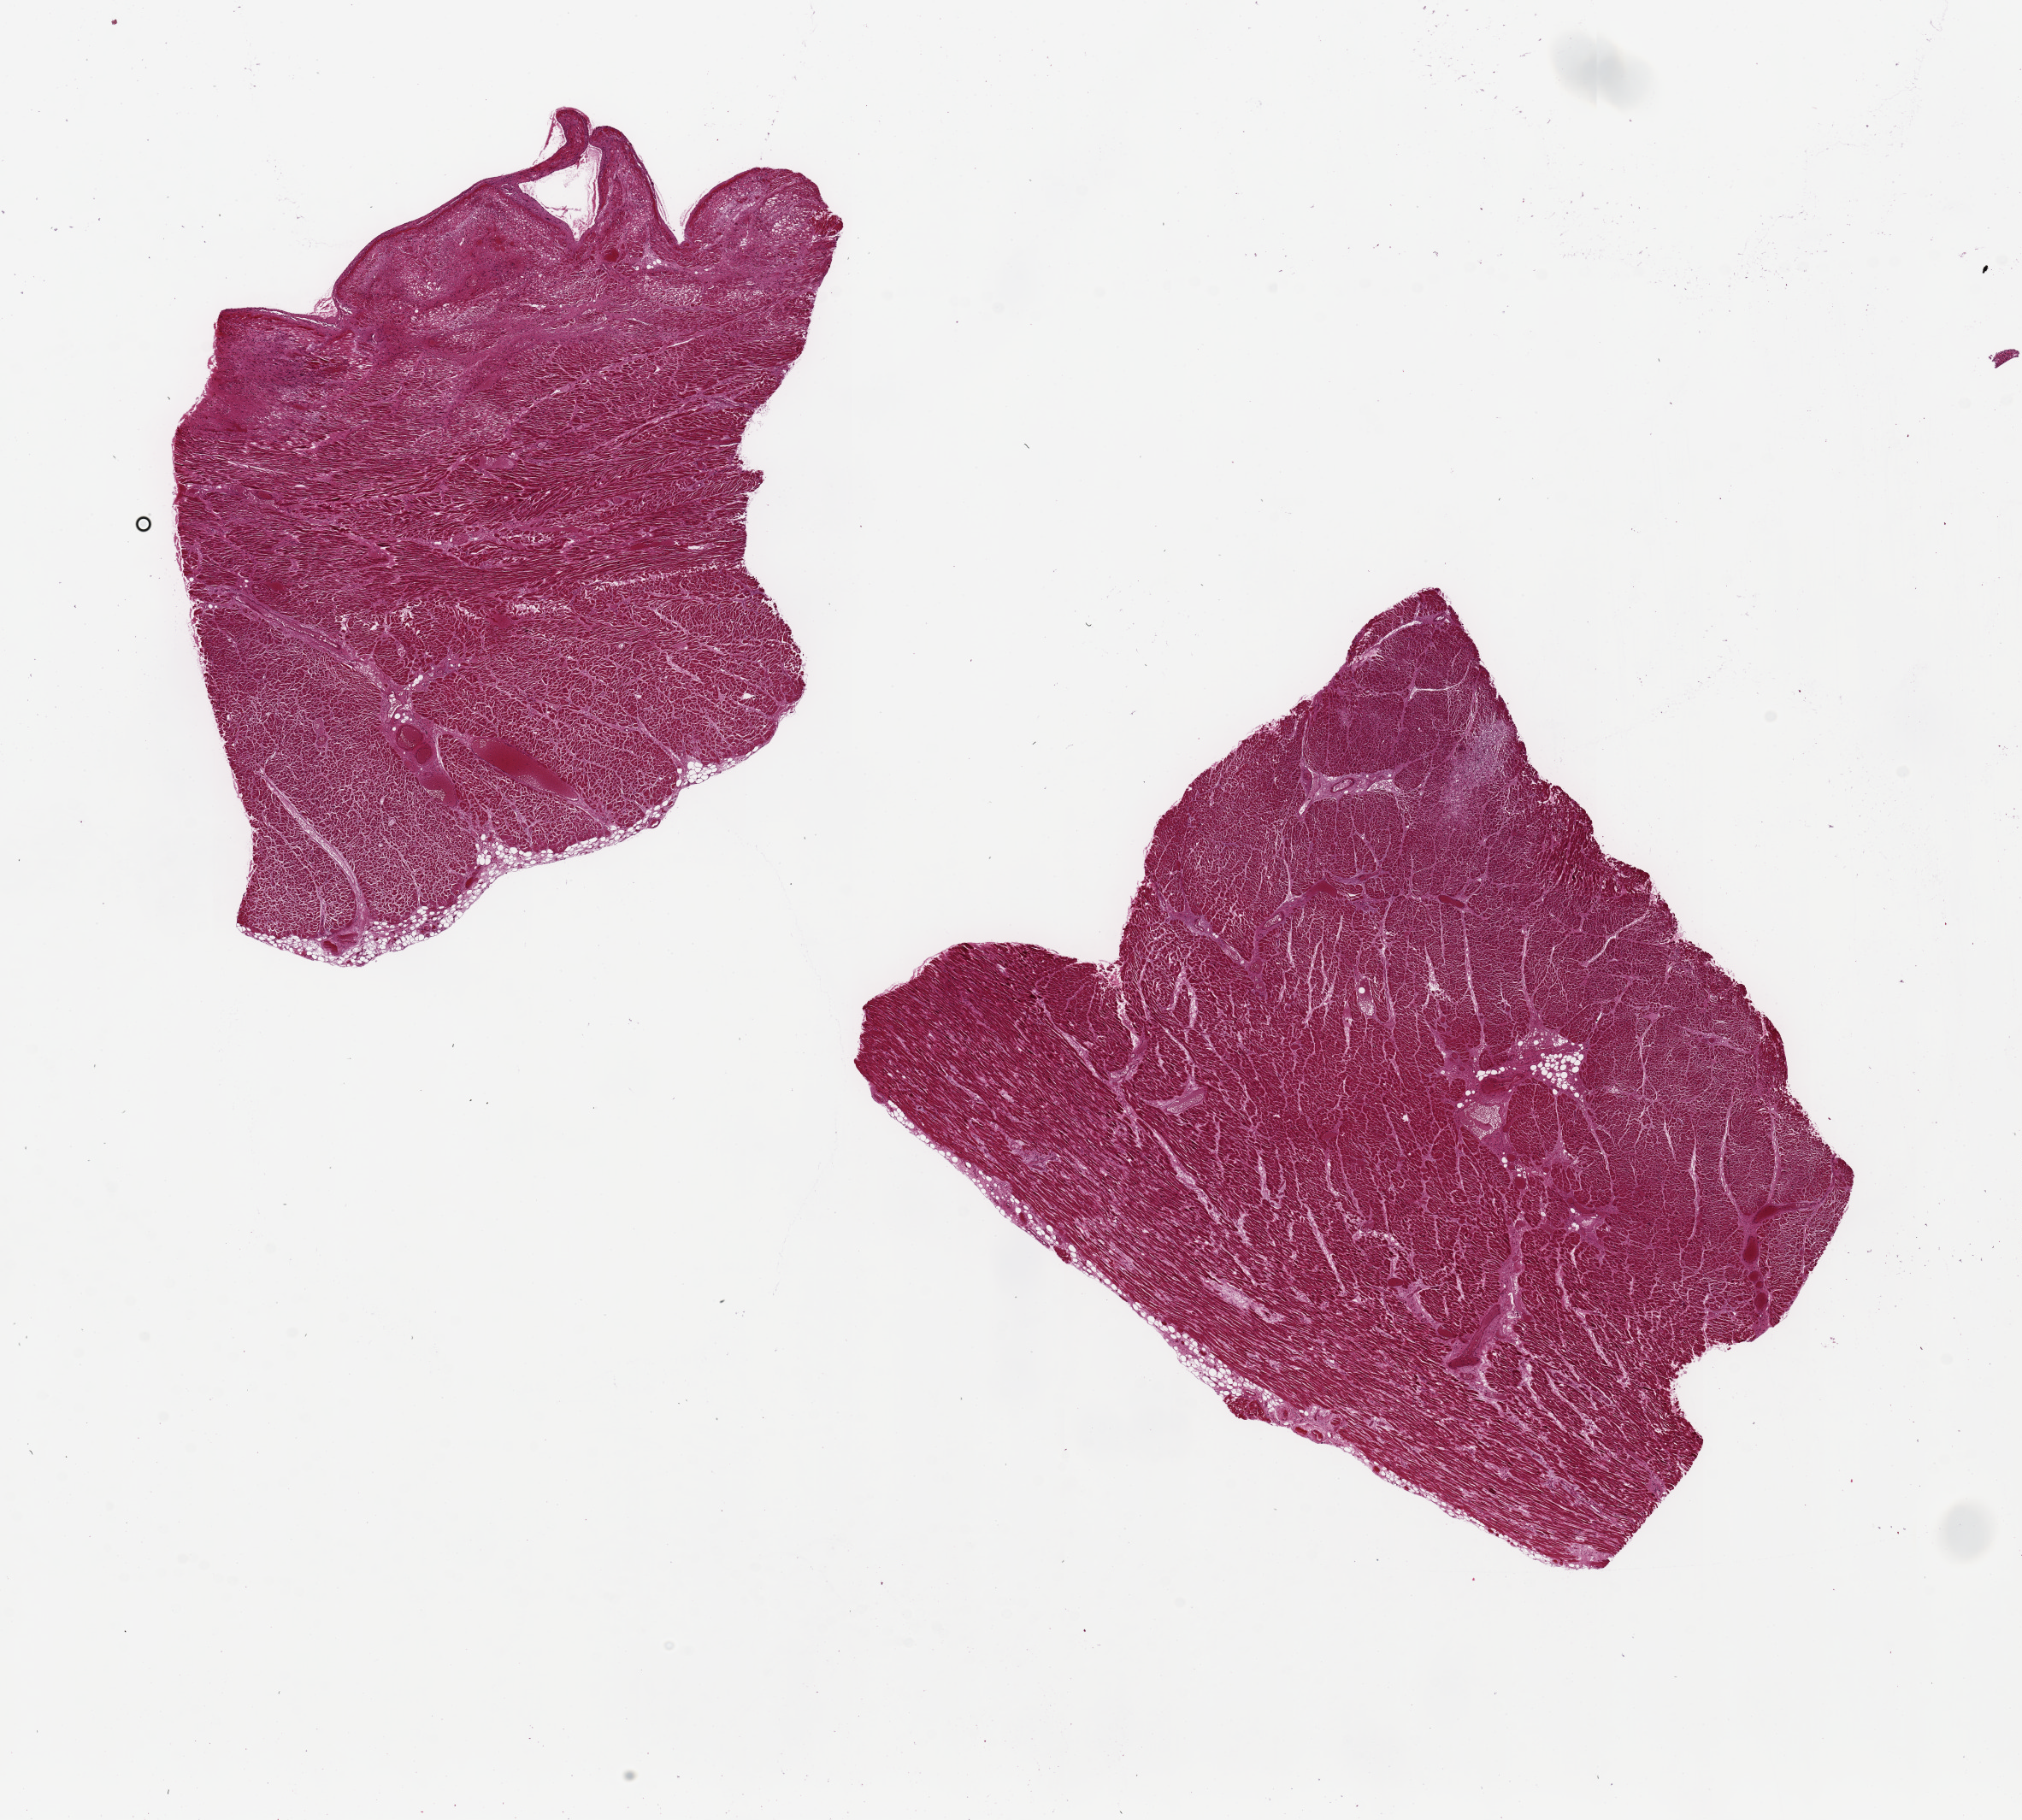
Whole-slide image, haematoxylin and eosin stain, brightfield, shown as a low-resolution overview of the whole scanned area (about 18.7 x 16.8 mm). PAXgene-fixed, paraffin-embedded tissue. Section of heart (target tissue). Donor tissue sample. Donor sex: male.
Reviewer comment on this tissue sample: 2 pieces, 8.5x7 & 8.5x6mm.